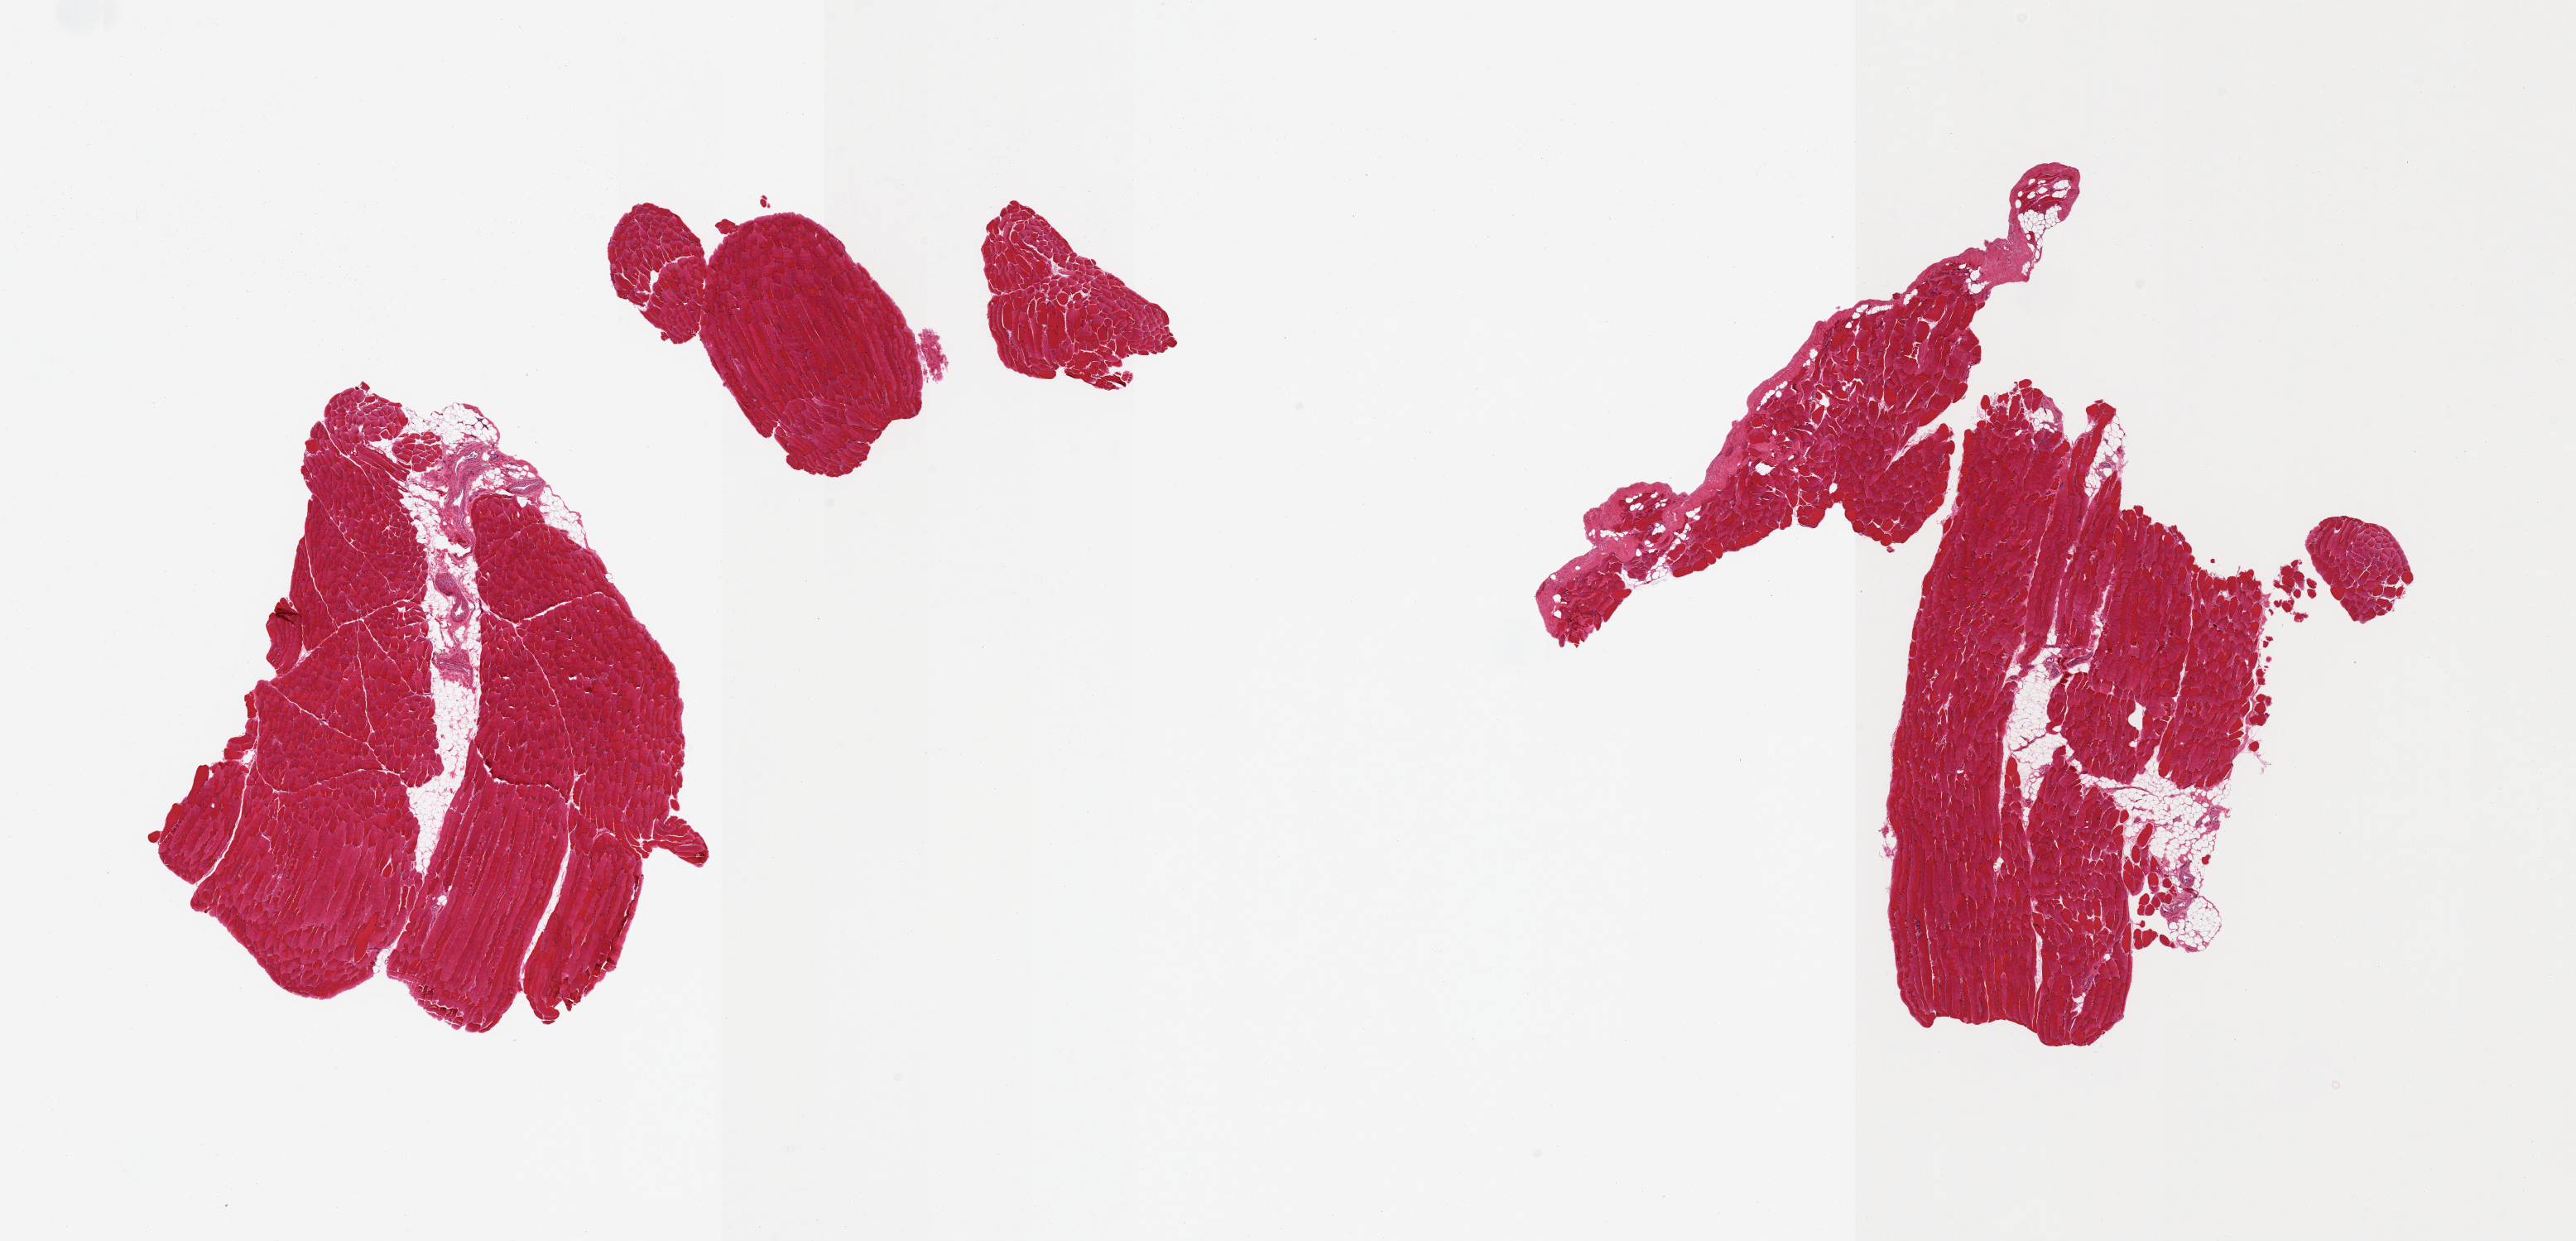
Whole-slide image, hematoxylin and eosin (H&E) stain, brightfield, whole scanned area (about 24.6 x 11.9 mm) shown as a low-resolution overview; PAXgene-fixed paraffin-embedded (PFPE) section; target tissue: skeletal muscle; tissue donor sample. Donor: male.
Pathologist's review note for this sample: 2 pieces, fragemented; ~5-10% interstitial fat/vascular elements.